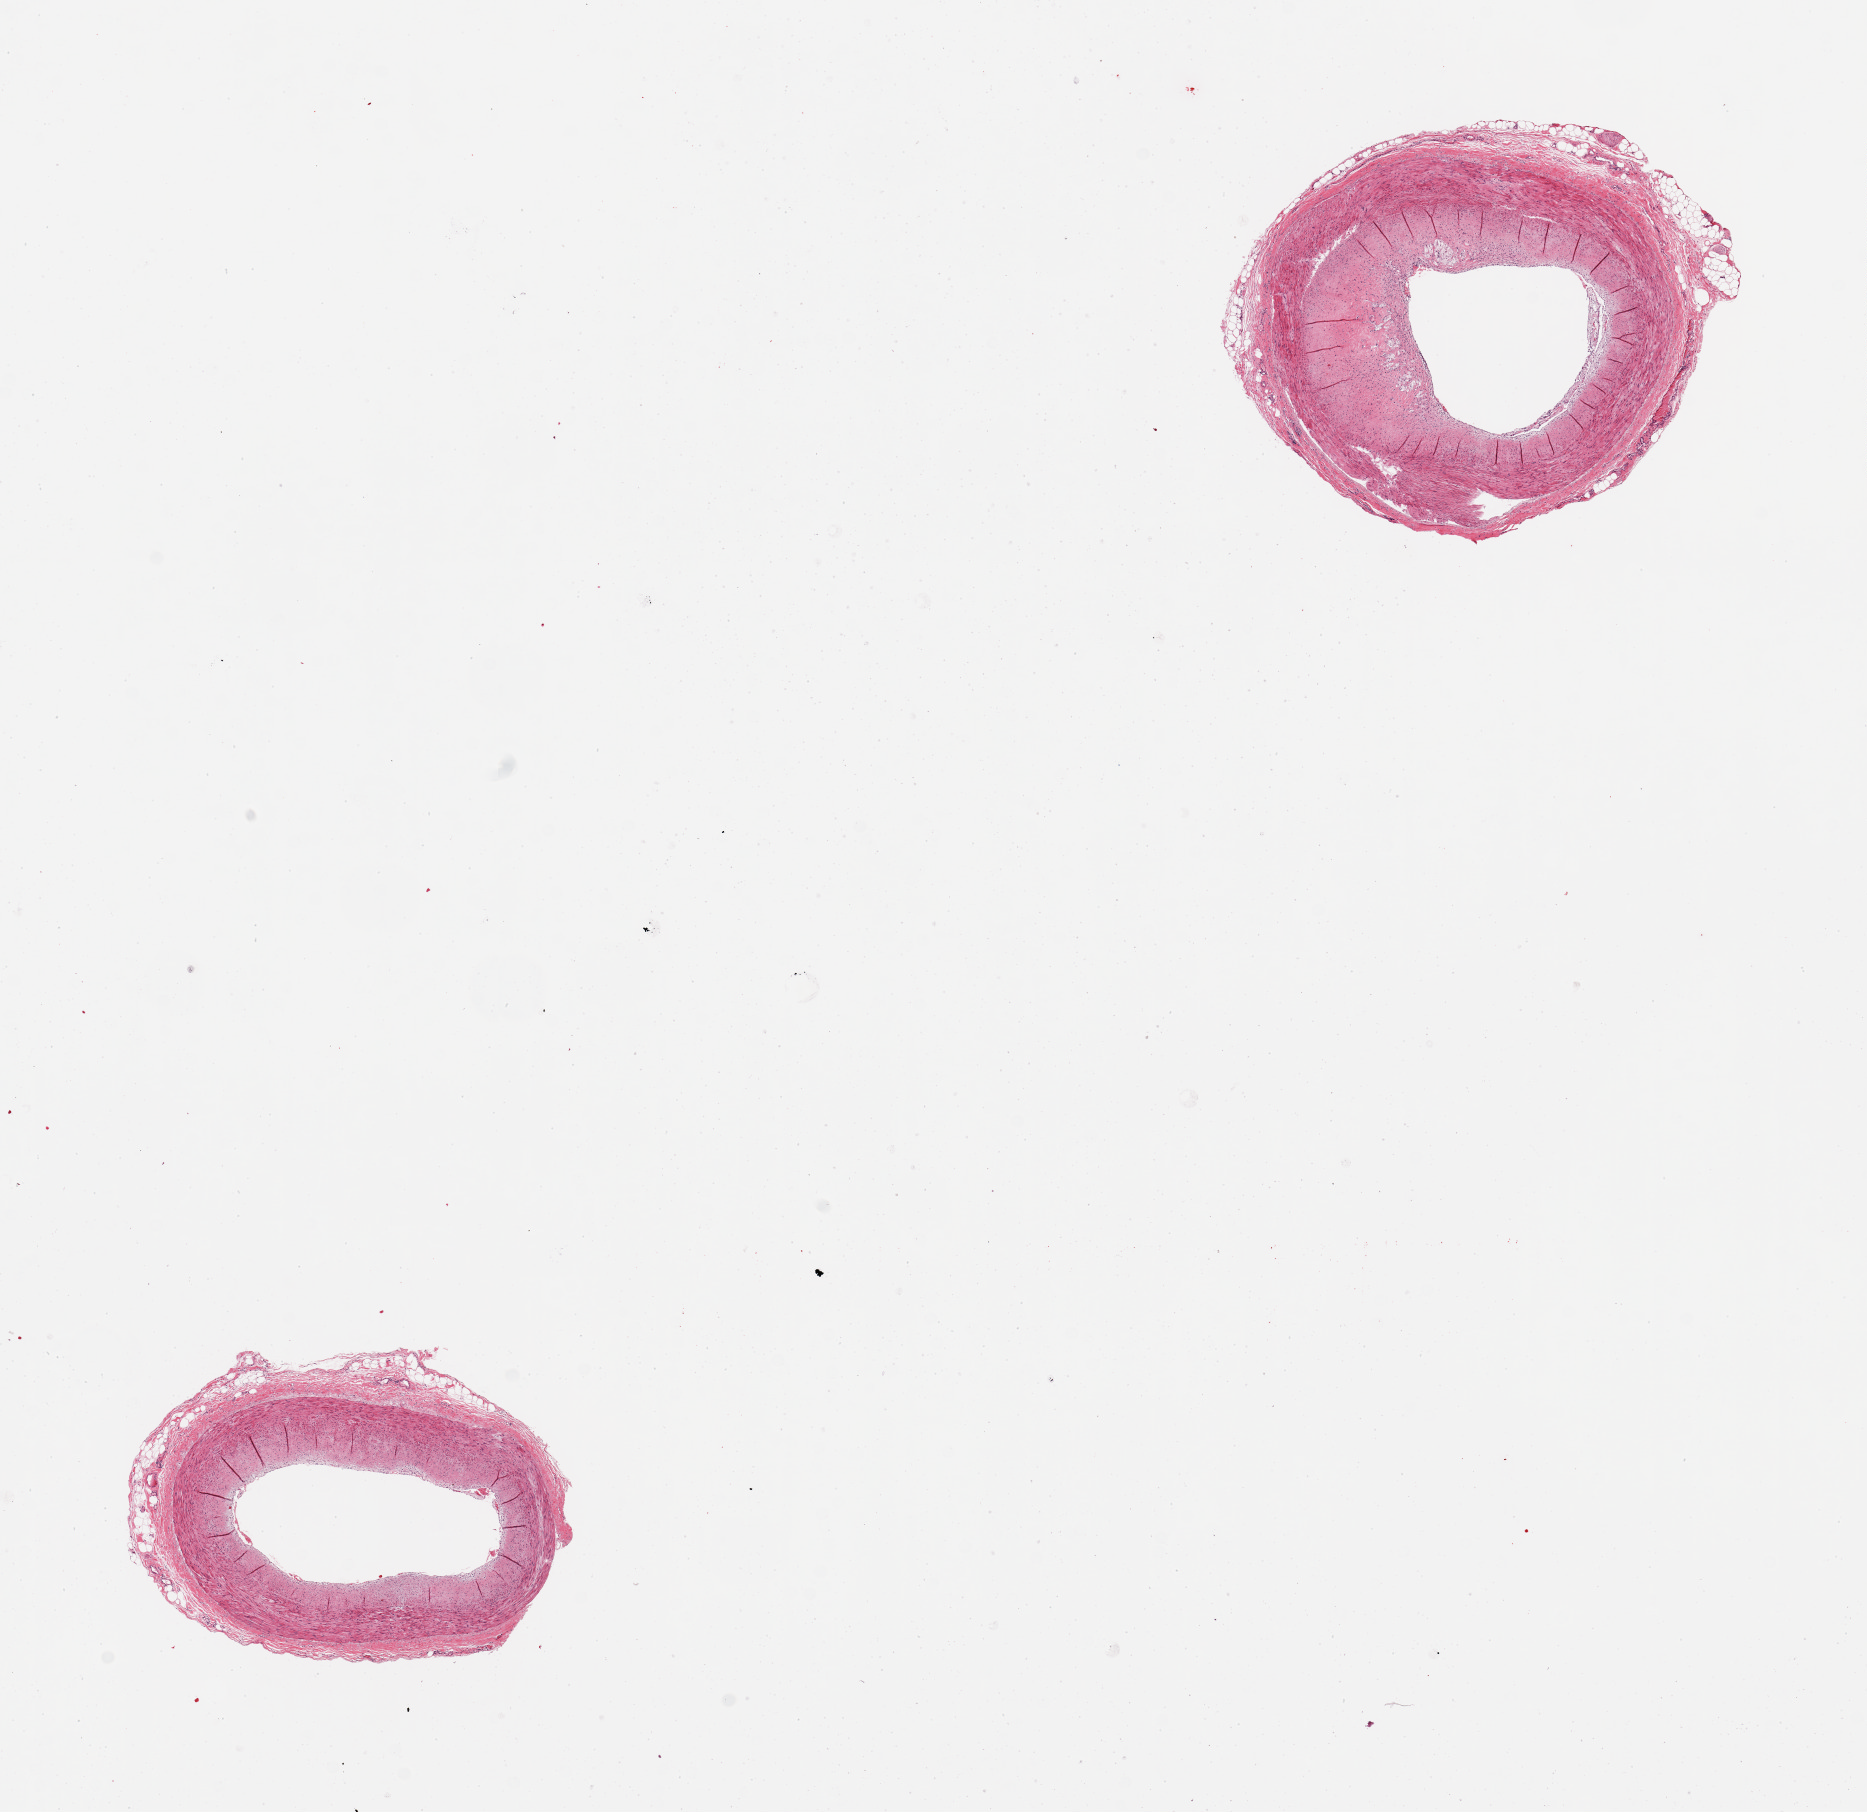
Haematoxylin and eosin whole-slide image, whole scanned area (about 14.8 x 14.3 mm, slide scanned at 20x) shown as a low-resolution overview. PAXgene-fixed, paraffin-embedded tissue. Section of coronary artery (target tissue). Tissue donor sample. Donor: male.
- reviewer comment on this tissue sample: 2 pieces. 1 with 30% fibrofatty plaque